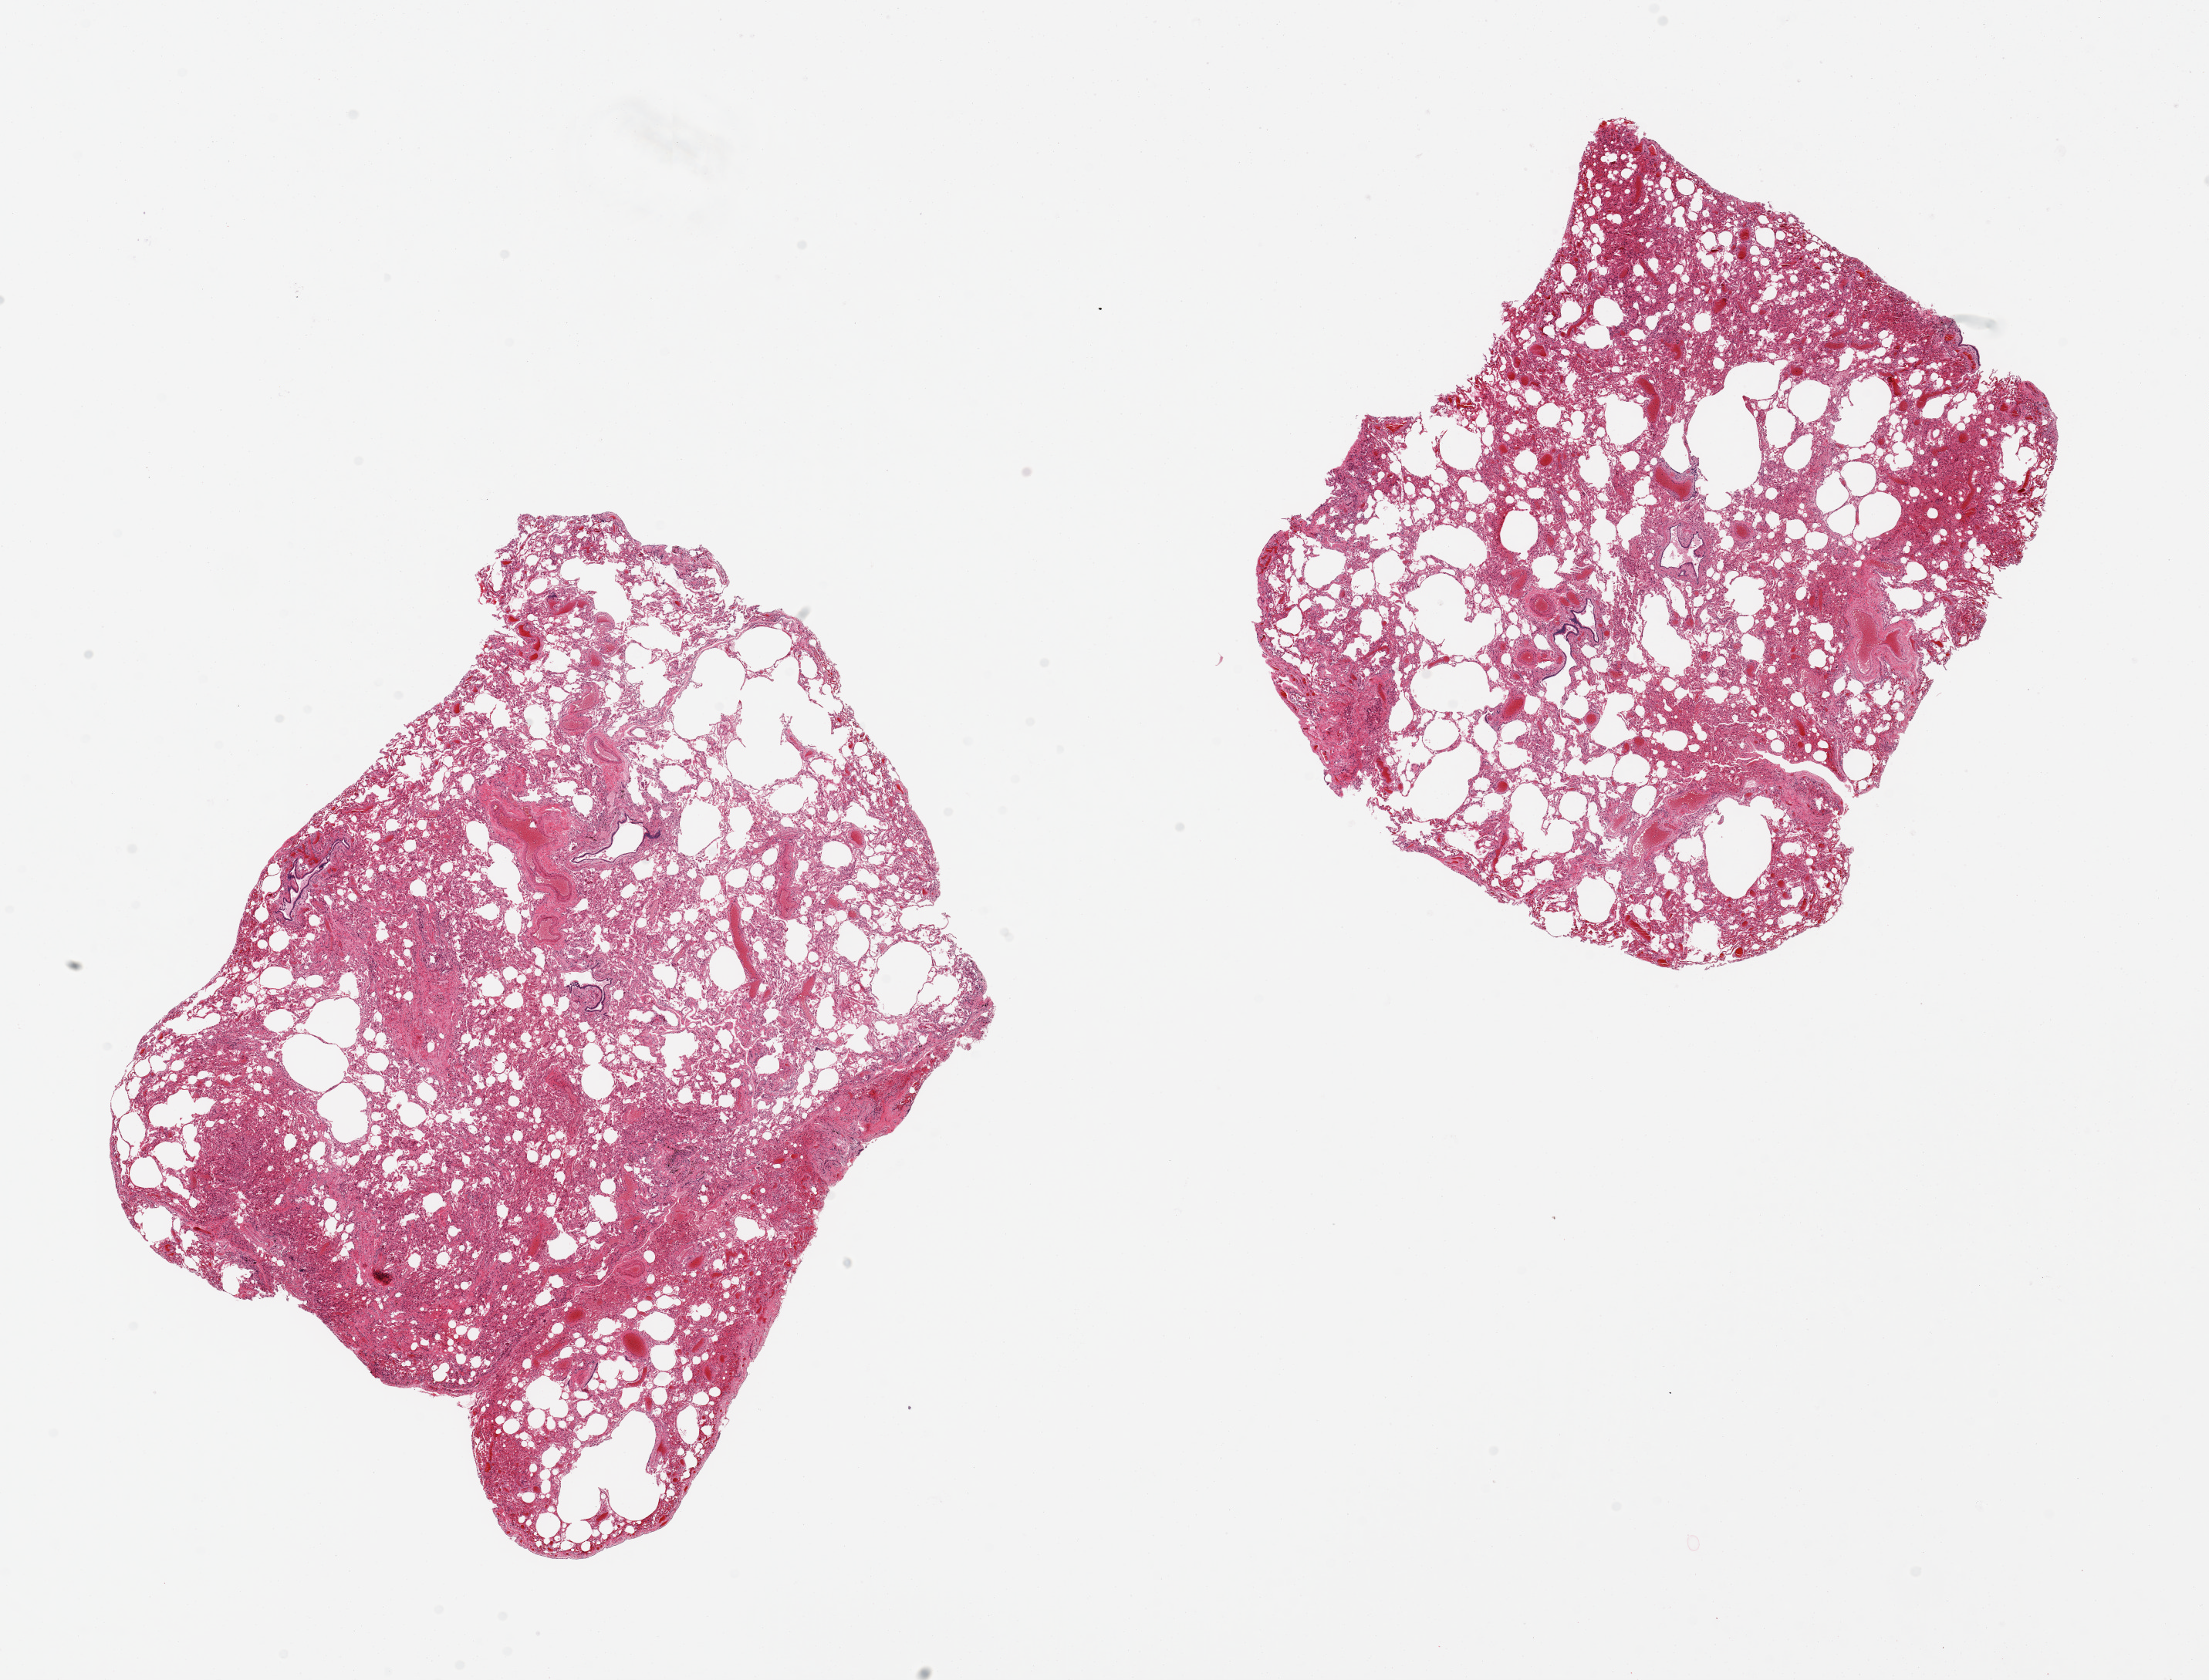
Hematoxylin and eosin (H&E) whole-slide image, low-resolution overview of the scanned area, about 22.6 x 17.2 mm (slide scanned at 20x); PAXgene-fixed paraffin-embedded (PFPE) section; section of lung (target tissue); tissue donor sample. Male donor.
Pathologist's review note for this sample: 2 pieces, 9x7 and 7x7mm; moderate congestion/atalectasis.